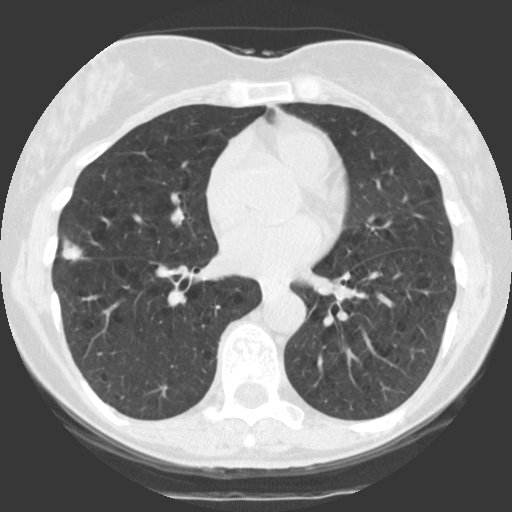
Chest CT (low-dose screening protocol), one axial image, baseline screening round, lung window (W 1500 / L -600 HU), 2.5 mm slice thickness, 140 kVp. Female participant, aged 68 years at enrolment. Former smoker at enrolment.
Lesion marked by an expert reader, box from (x=51, y=233) to (x=98, y=281) px. The screening reader recorded 2 non-calcified nodules or masses ≥4 mm on this exam (right lower lobe, right middle lobe); which of them this box marks is not recorded. Official screen result: positive, change unspecified: nodule(s) >= 4 mm or enlarging nodule(s), mass(es), or other non-specific abnormalities suspicious for lung cancer. Lung cancer was diagnosed 40 days after this screen: bronchiolo-alveolar adenocarcinoma, NOS, right upper lobe, right middle lobe, right lower lobe, well differentiated (G1), stage IV (AJCC 6th edition).